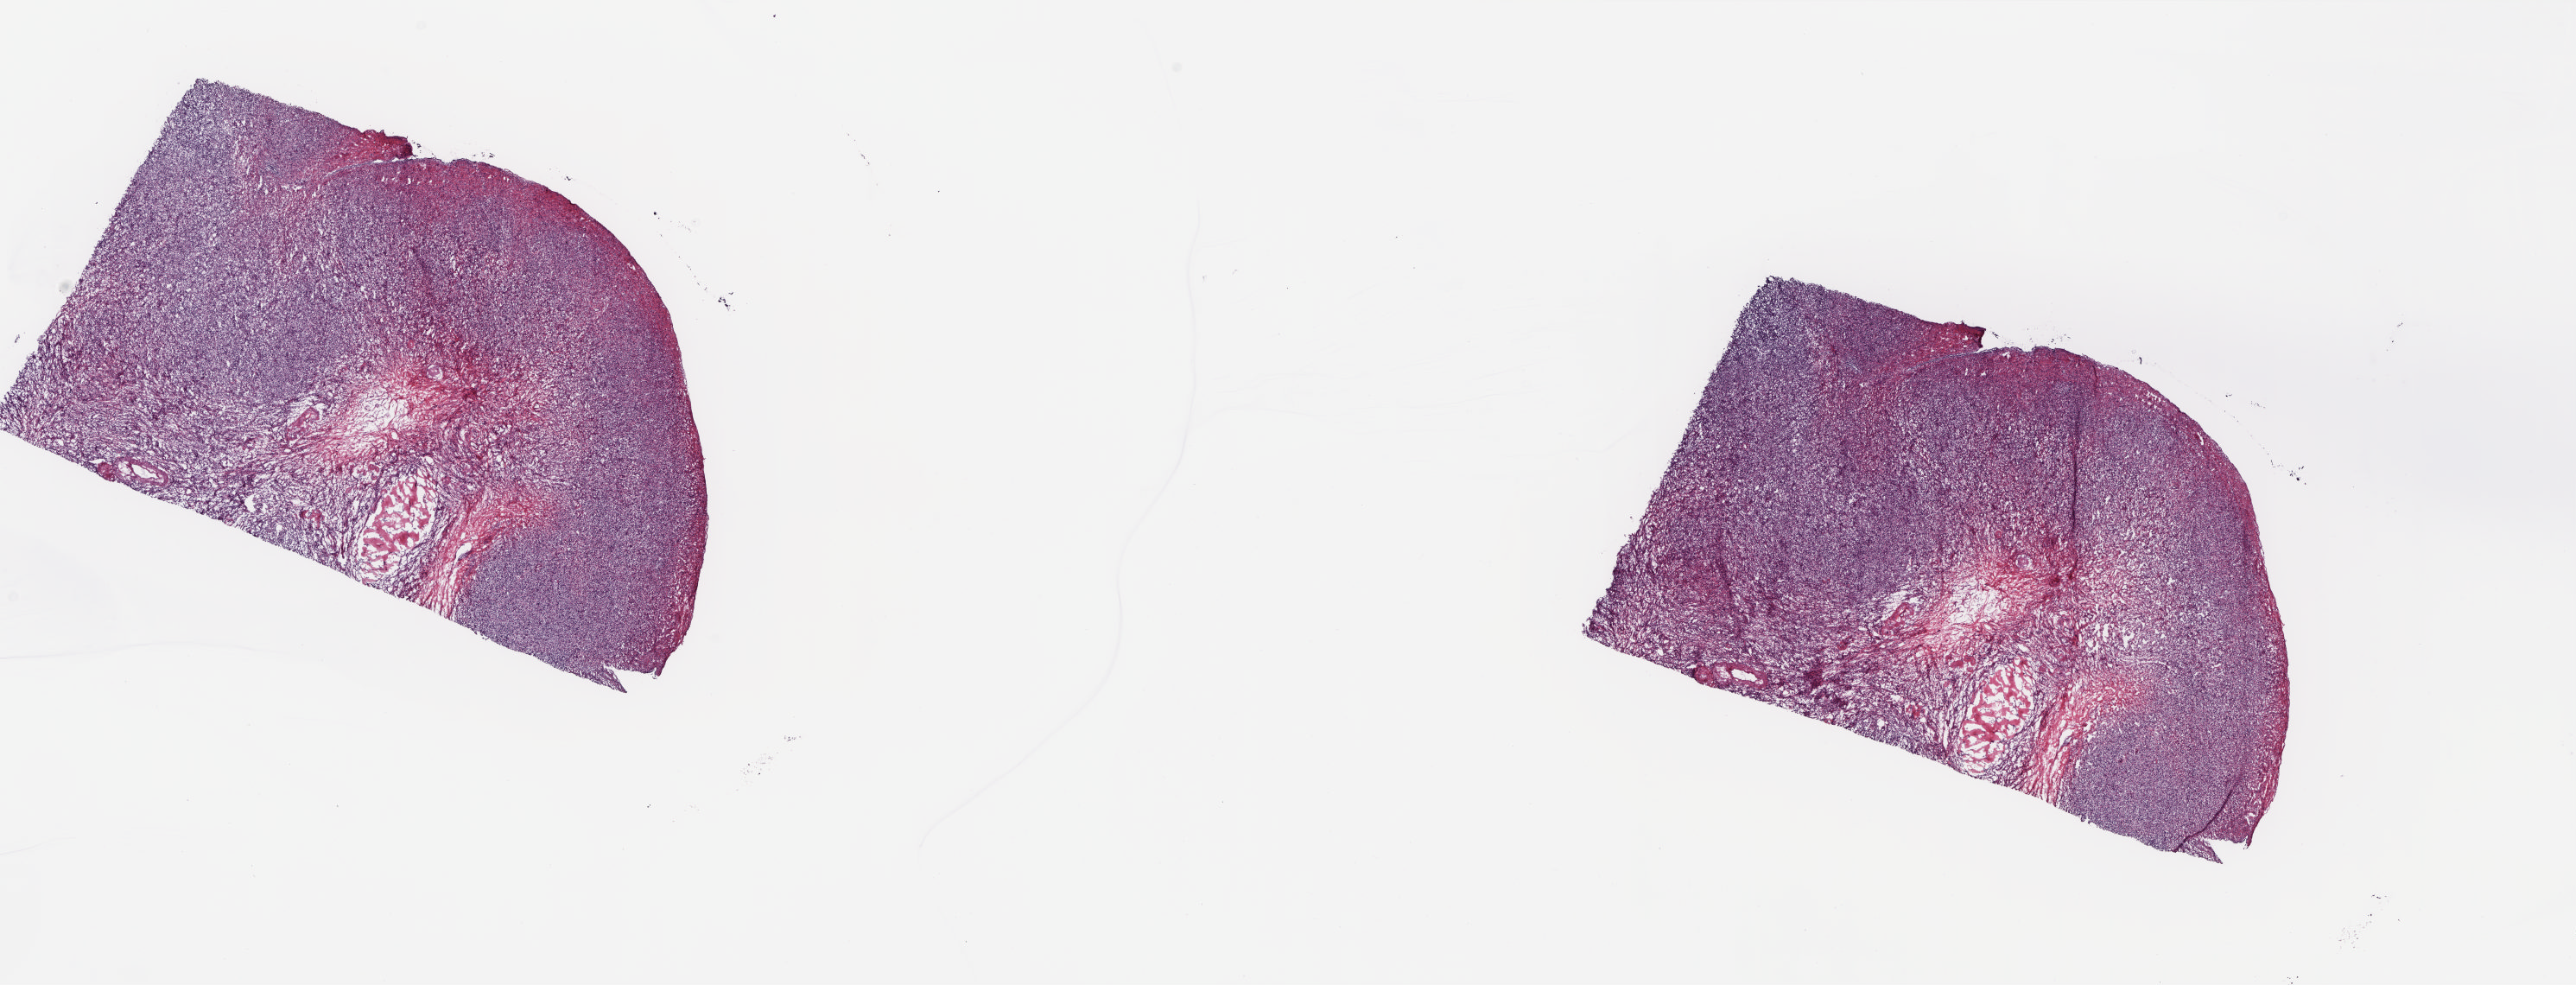
Whole-slide histology image, Hematoxylin and eosin (H&E) stained — whole scanned area (about 24.0 x 9.2 mm, acquisition: 20x scan) shown as a low-resolution overview, frozen section from the top of the tissue portion, solid tissue normal (non-tumour tissue) sample from the uterus. Female, age 83 years at initial diagnosis. Composition of this section per pathologist review: tumour cells 0%, tumour nuclei 0%, normal cells 100%, stromal cells 0%, necrosis 0%. Inflammatory infiltration, as recorded: lymphocyte infiltration 0%, monocyte infiltration 0%, neutrophil infiltration 0%.
* this section: solid tissue normal sample (biorepository sample class)
* patient diagnosis: Mullerian mixed tumor (endometrium)